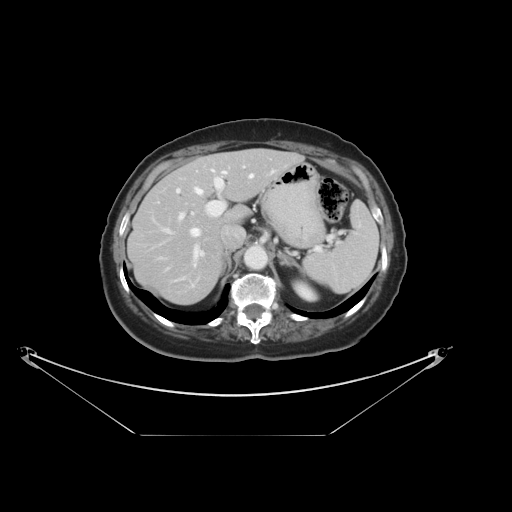
Contrast-enhanced abdominal CT, one axial slice. Position 24 of 36 along the scan axis. Reconstruction kernel STANDARD. Intravenous contrast given. Soft-tissue window (W 400 / L 40 HU). 512 × 512 image matrix. Female patient, age 70 years. Case-level facts recorded for this patient, not image findings: diagnosis: colorectal cancer liver metastases, imaged before liver resection; multiple liver metastases: no; largest metastasis: 2.5 cm; disease in both lobes: no.
Annotated regions visible in this slice (expert manual segmentation):
- hepatic veins: bounding box <141,169,254,250> (left, top, right, bottom; pixels)
- liver: <129,150,300,306>
- planned liver remnant (the part of the liver to remain after resection): <129,150,300,305>
- portal vein (with intrahepatic branches): <175,170,226,268>